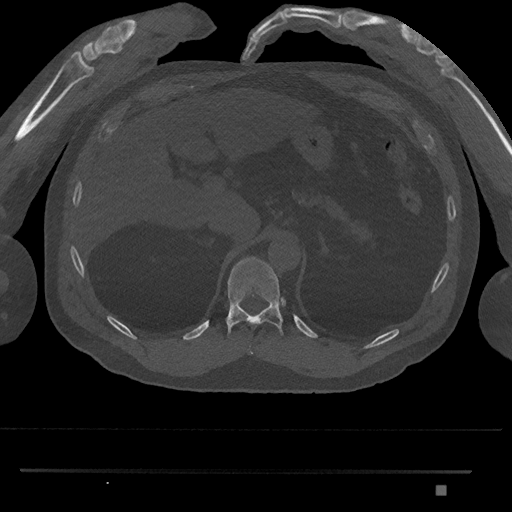
CT including the spine, one axial slice; position 950 of 1134 along the scan axis; reconstruction kernel Br40s/3; 120 kVp; bone window (W 1800 / L 400 HU); 512 × 512 image matrix, field of view 429 × 429 mm. Patient: male, 65 years. From the clinical record (not read from this slice): primary cancer: prostate.
Outlined on this slice (semi-automatically segmented with operator editing):
- T10 vertebra: bounding box <249,351,253,354> (left, top, right, bottom; pixels)
- T11 vertebra: <226,256,284,335>